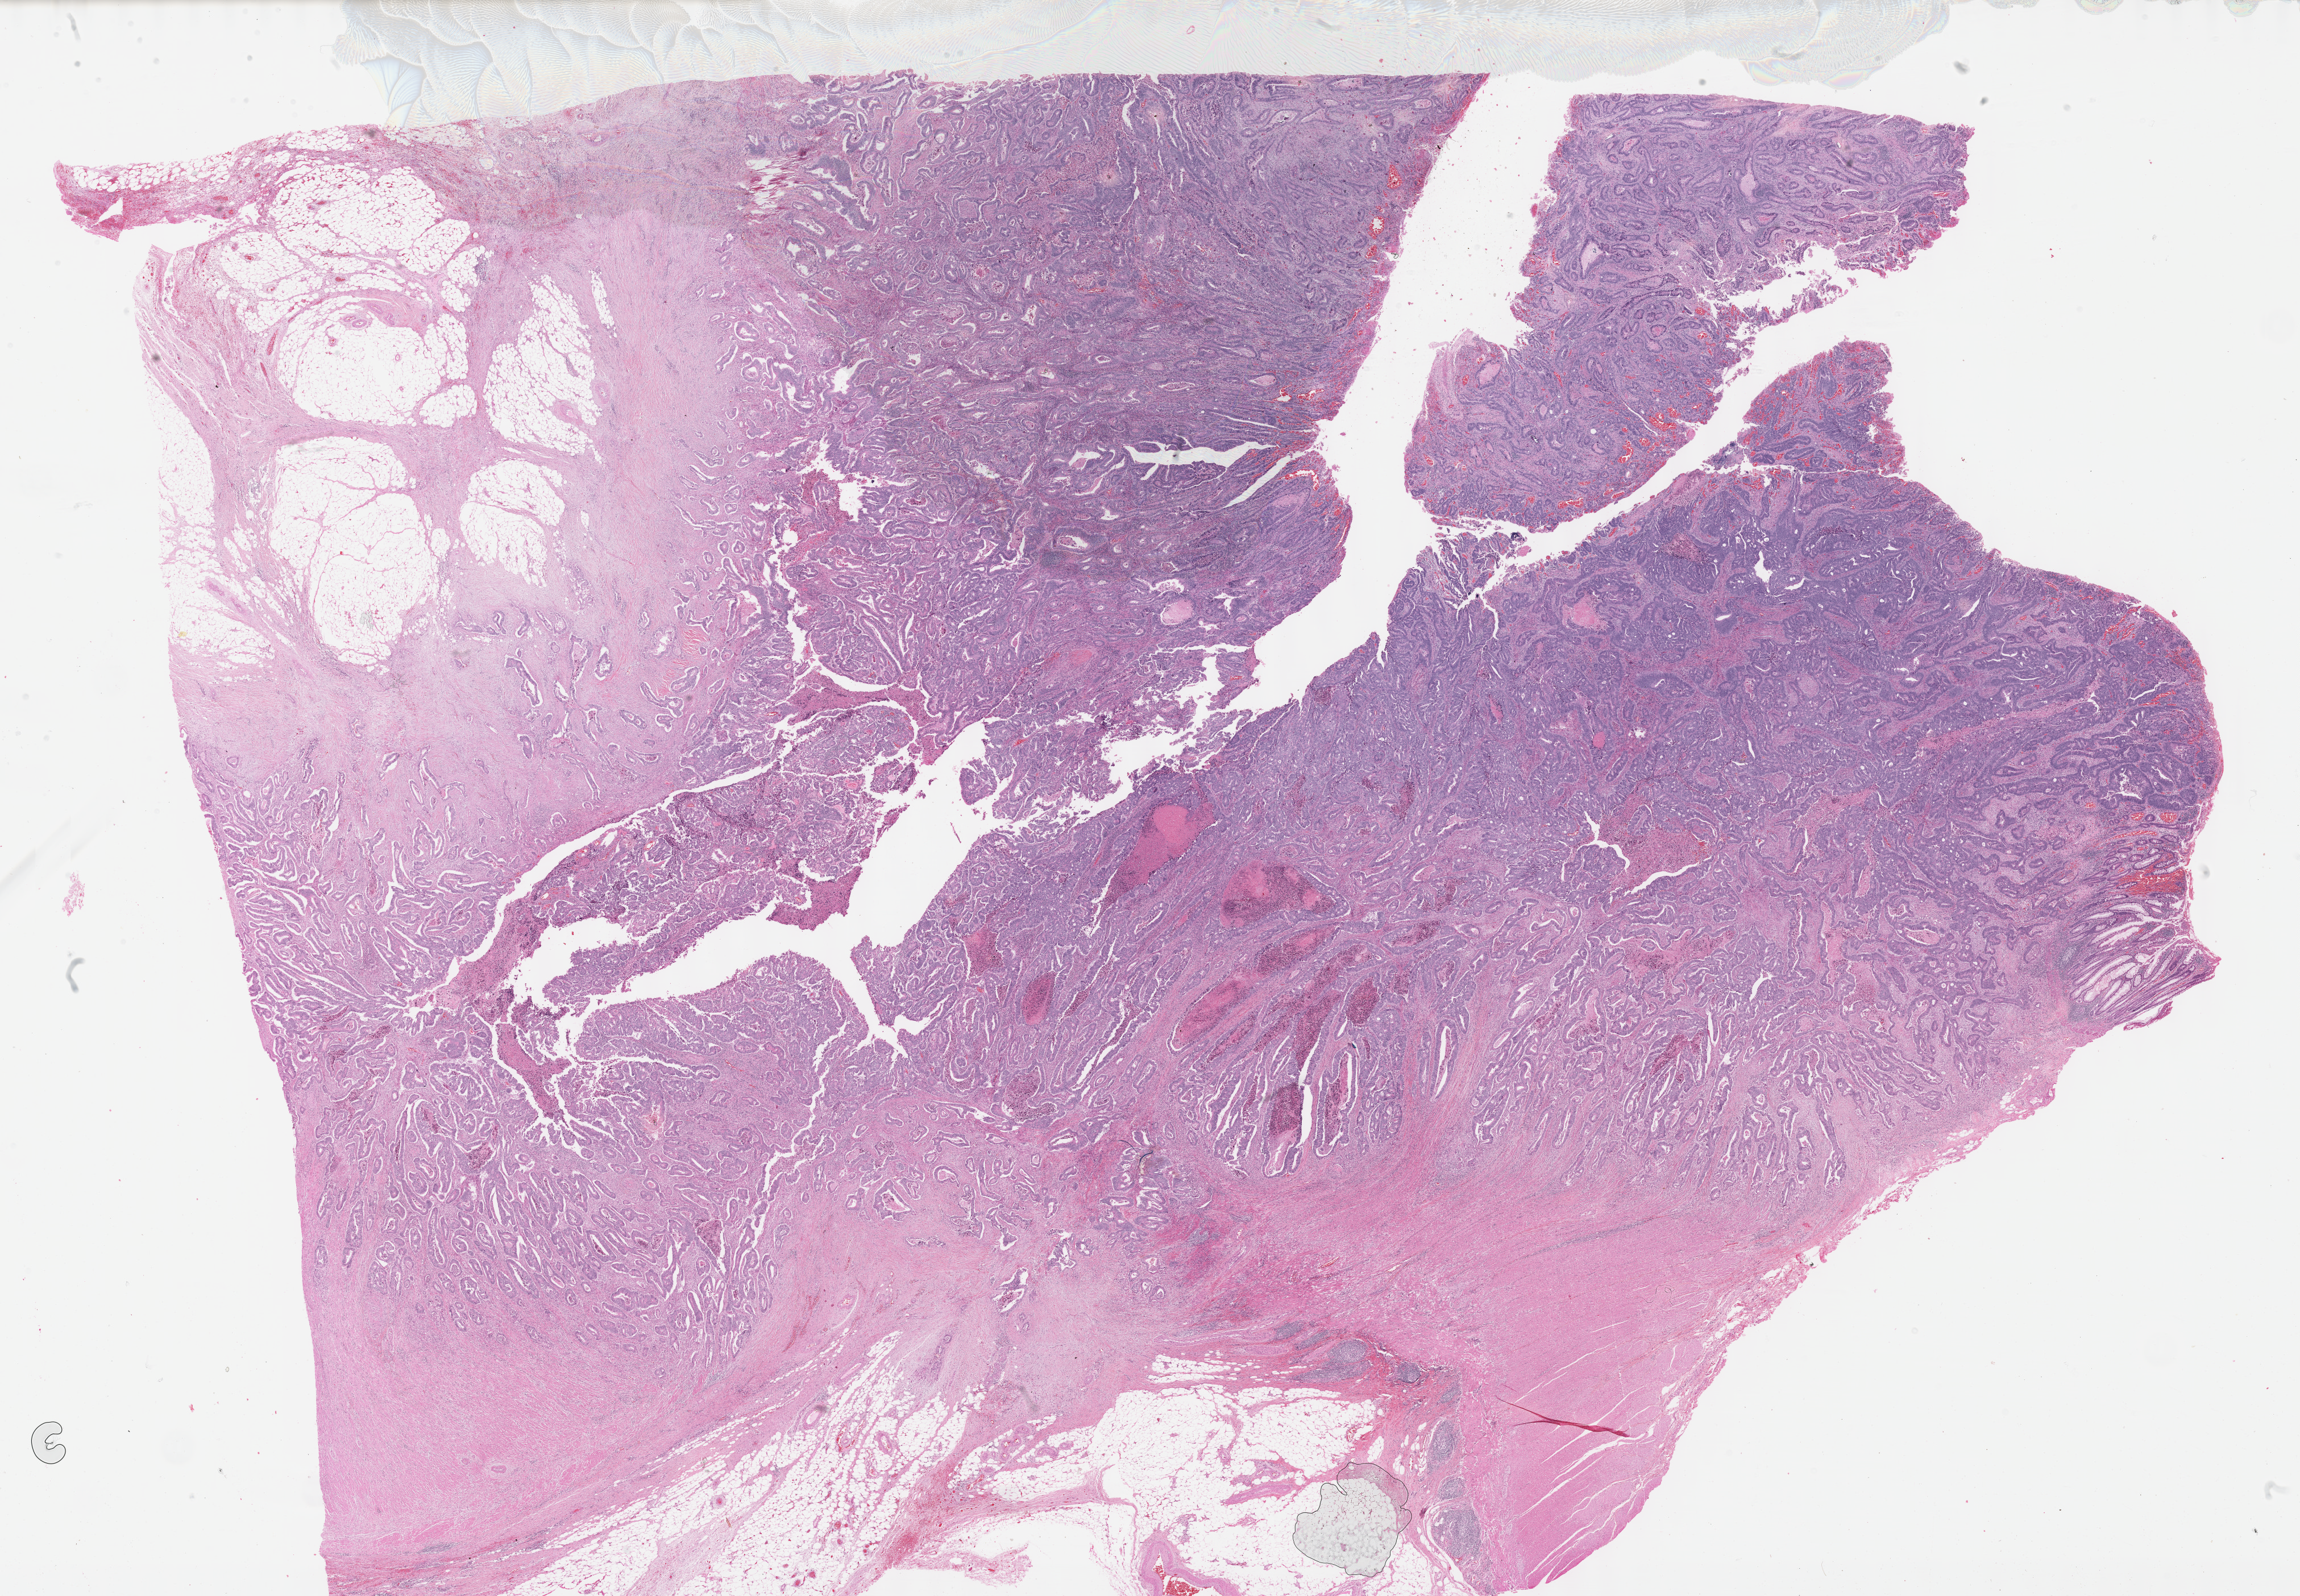
H&E-stained whole-slide image — low-resolution overview of the scanned area, about 32.7 x 22.7 mm; formalin-fixed paraffin-embedded (FFPE) diagnostic section; primary tumour sample from the colon. Male, age 76 years at initial diagnosis.
TNM: T3 N0 M0. Lymph nodes positive (case pathology): 0 of 15 examined. Histologic diagnosis: Adenocarcinoma, NOS (ascending colon). AJCC pathologic stage: IIA (7th edition).